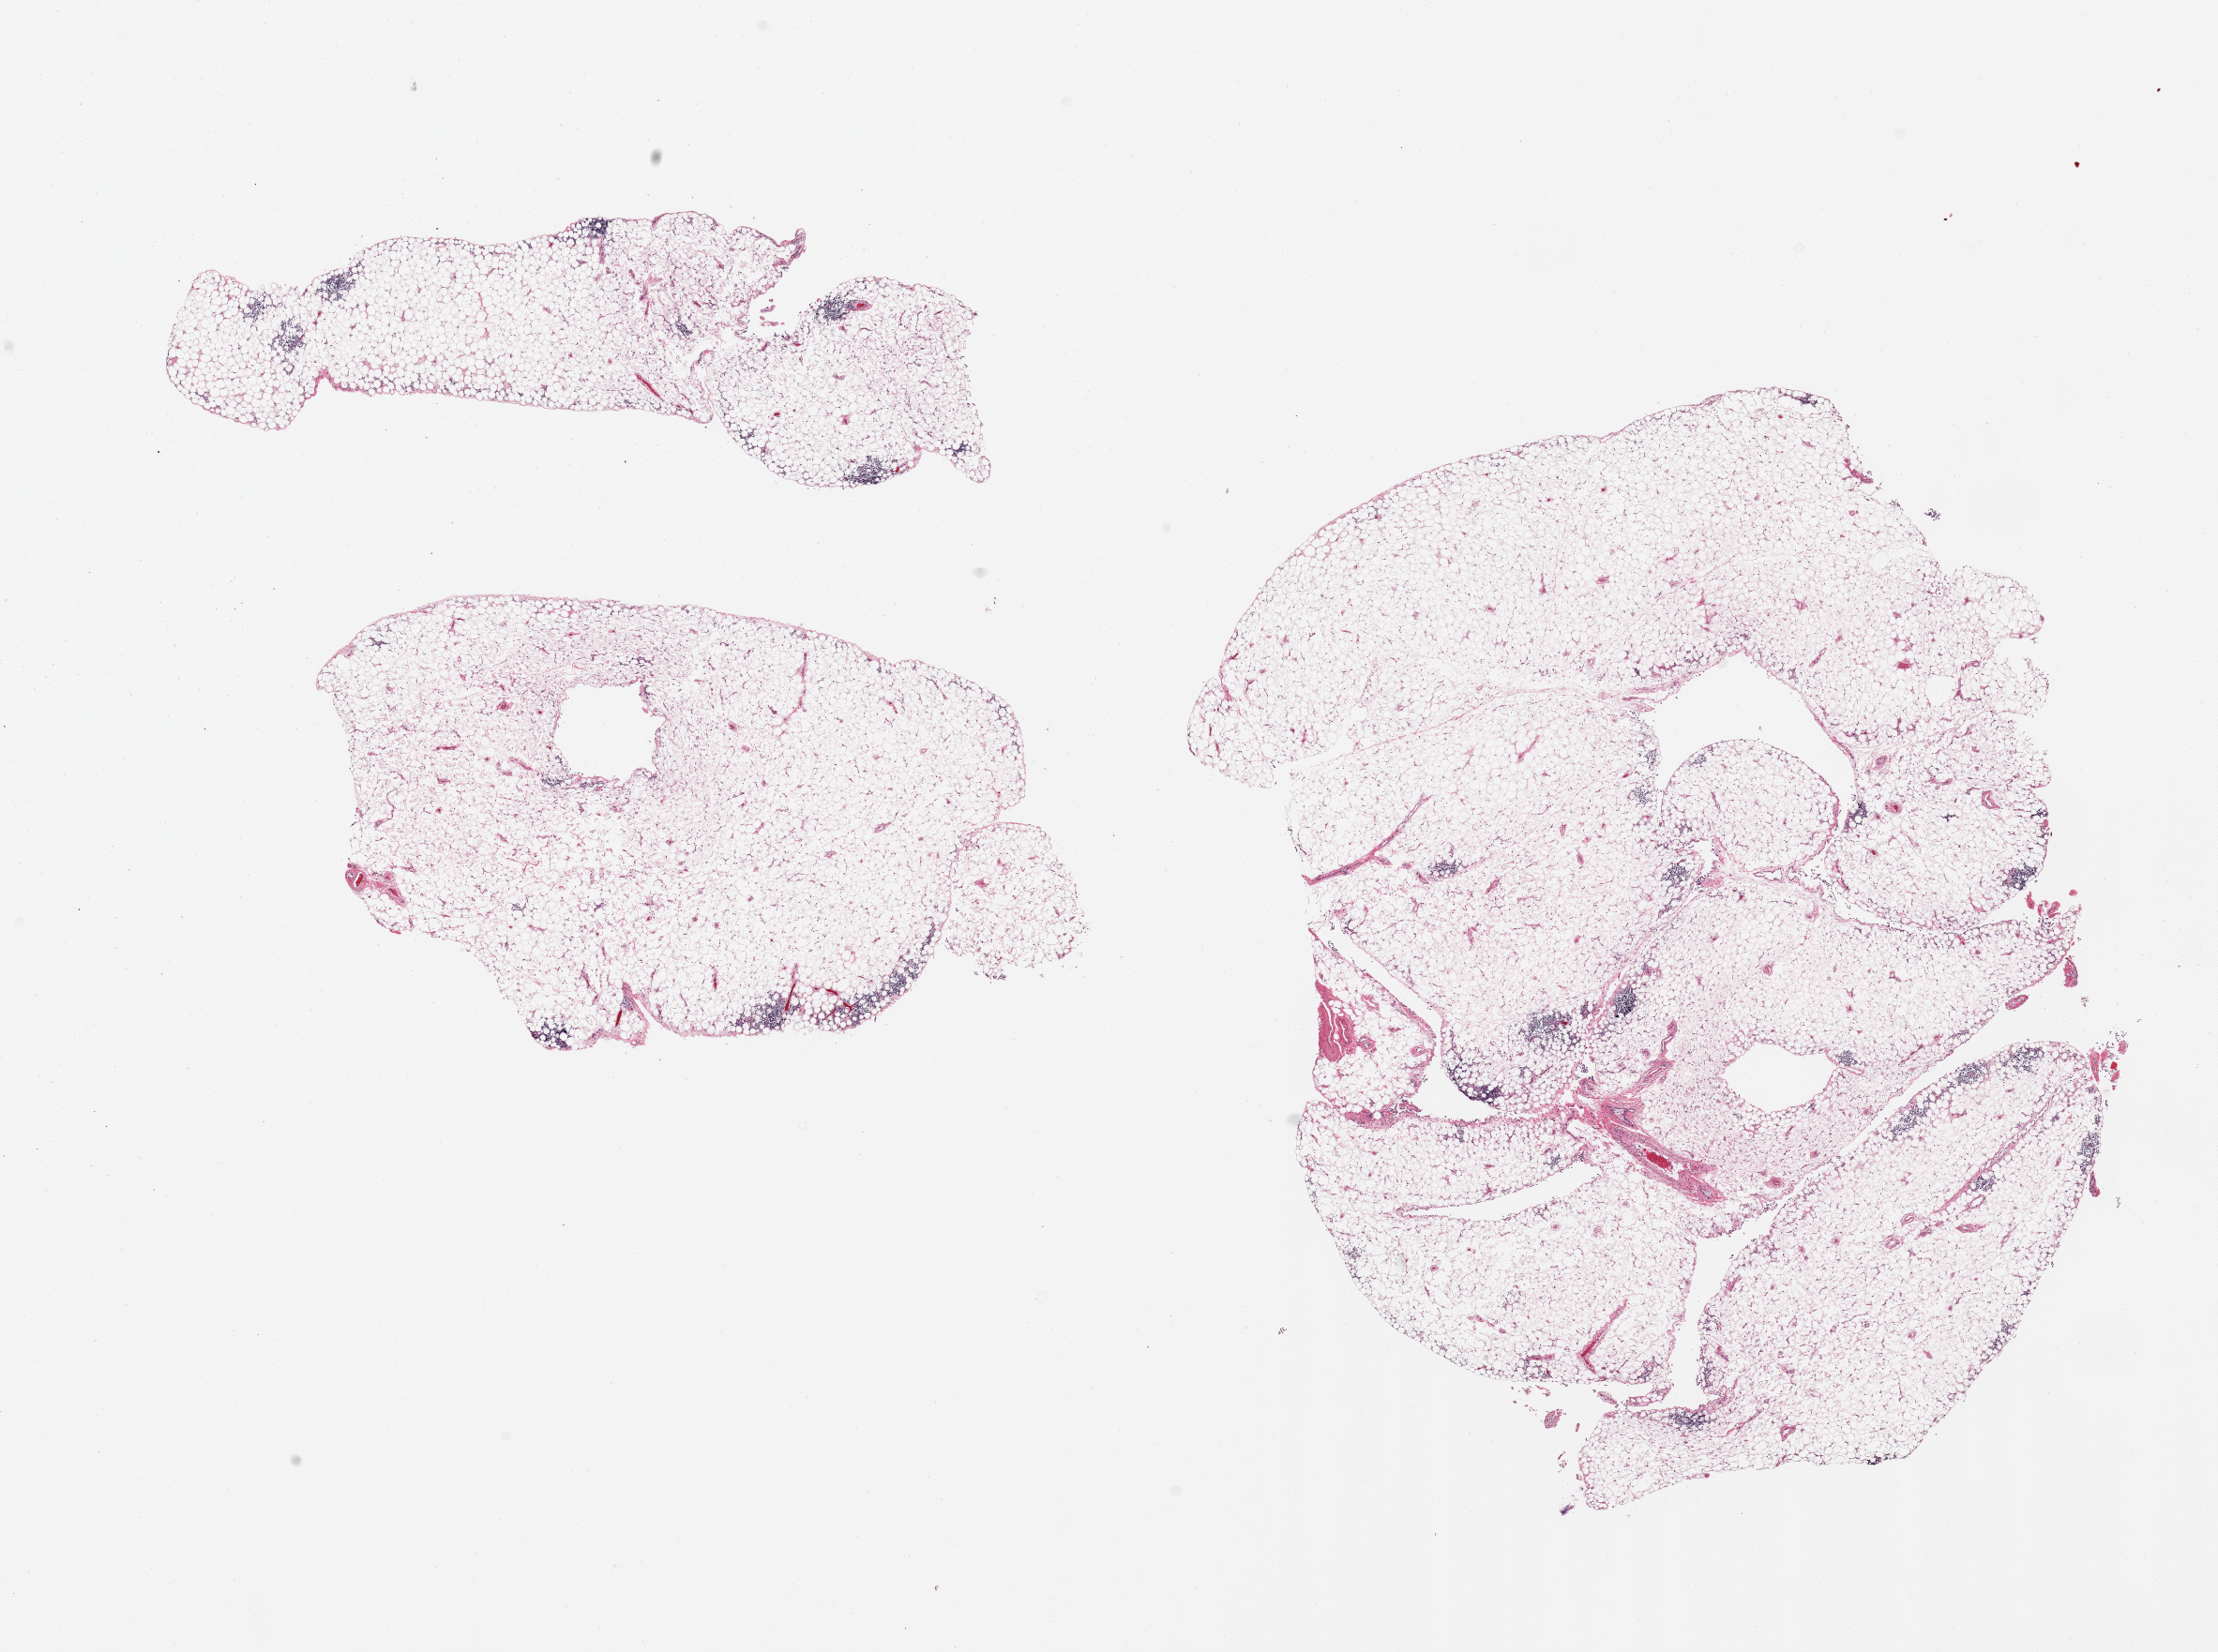
Digitized hematoxylin and eosin (H&E)-stained section — whole scanned area (about 18.7 x 13.9 mm) shown as a low-resolution overview. PAXgene-fixed, paraffin-embedded tissue. Target tissue: omentum. Donor tissue sample. Donor: male.
Reviewer comment on this tissue sample: 2 pieces, patchy chronic inflammation.